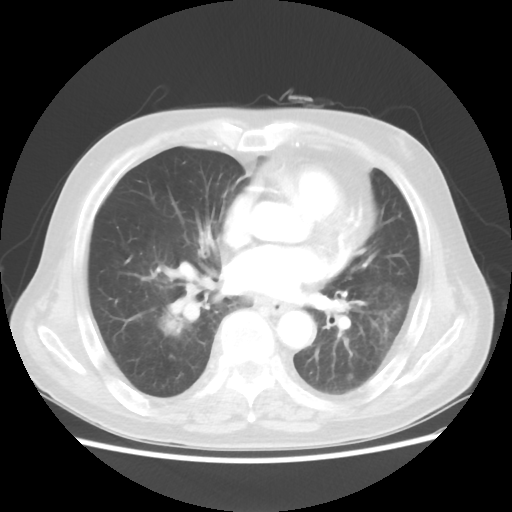
Chest CT, one axial slice; position 17 of 44 along the scan axis; 100 kVp; lung window (W 1500 / L -600 HU); 5 mm slice thickness; 512 × 512 image matrix, field of view 359 × 359 mm. Male patient, age 83 years. Case-level facts recorded for this patient, not image findings: clinical TNM (as recorded): T2 N3 M0.
Structures marked on this image (rectangle marked by the reading radiologist):
- lung tumour (recorded histology: adenocarcinoma): bounding box (x1, y1, x2, y2) in pixels: (158, 295, 197, 356)